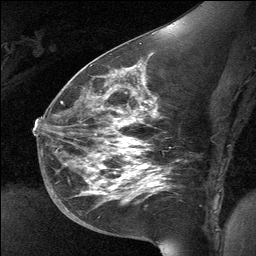
Breast MRI (dynamic contrast-enhanced), one sagittal slice. Slice 35 of 64 in the series (ordered by position). Dynamic contrast-enhanced study with each time point stored as its own series, time point 2 of 3 at this slice position (early post-contrast, ordered by acquisition time). 1.5 T. TE 4.8 ms, TR 27 ms. 2 mm slice thickness. 256 × 256 image matrix, field of view 200 × 200 mm. Patient: female, 39 years. From the clinical record (not read from this slice): setting: breast cancer imaged before/during neoadjuvant chemotherapy; receptor status: HER2-positive.
Annotated regions visible in this slice (semi-automatic segmentation, software-assisted and operator-edited):
- analysis volume of interest (the breast-tissue region the enhancement analysis was run in; not a lesion): box from (x=70, y=69) to (x=163, y=224) px
- tumour enhancement mask (voxels above the 90 % enhancement threshold inside the analysis volume of interest): (x=90, y=69)–(x=158, y=193)